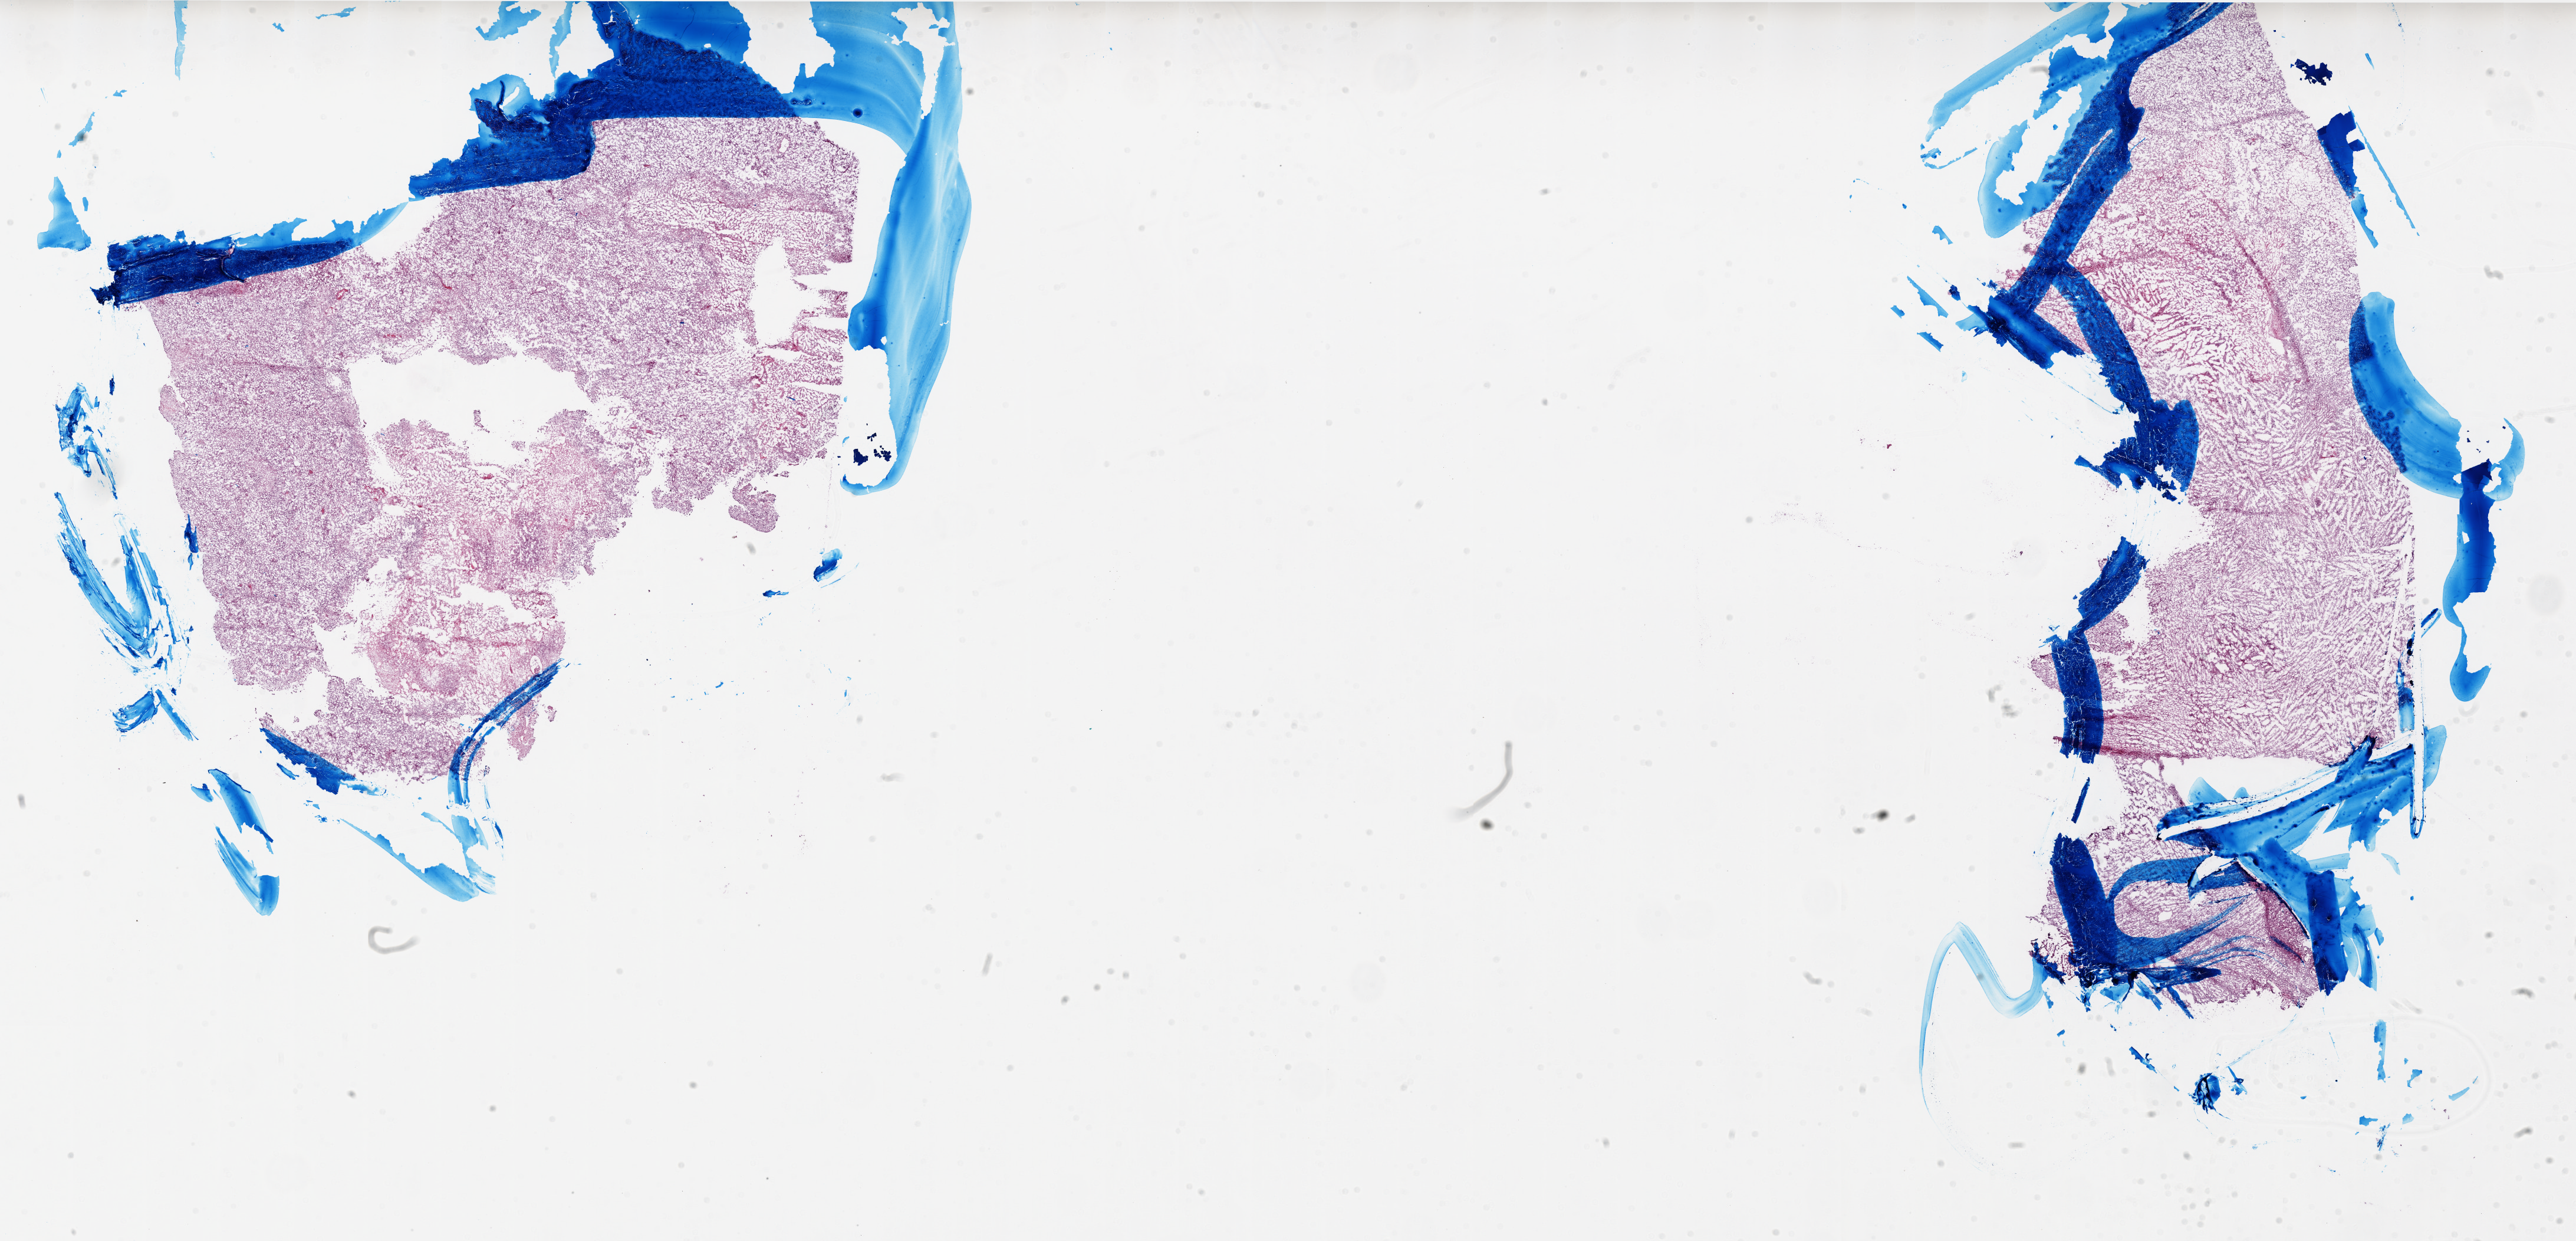
Digitized H&E tissue section (whole slide) — low-resolution overview of the scanned area, about 35.0 x 16.8 mm (from a 20x scan); frozen section; brain, primary tumour sample. Female patient; age at initial diagnosis 45 years. Pathologist review of this section (percent, as recorded): tumour cells 80%, tumour nuclei 100%, normal cells 0%, stromal cells 0%, necrosis 20%.
- diagnosis: Glioblastoma